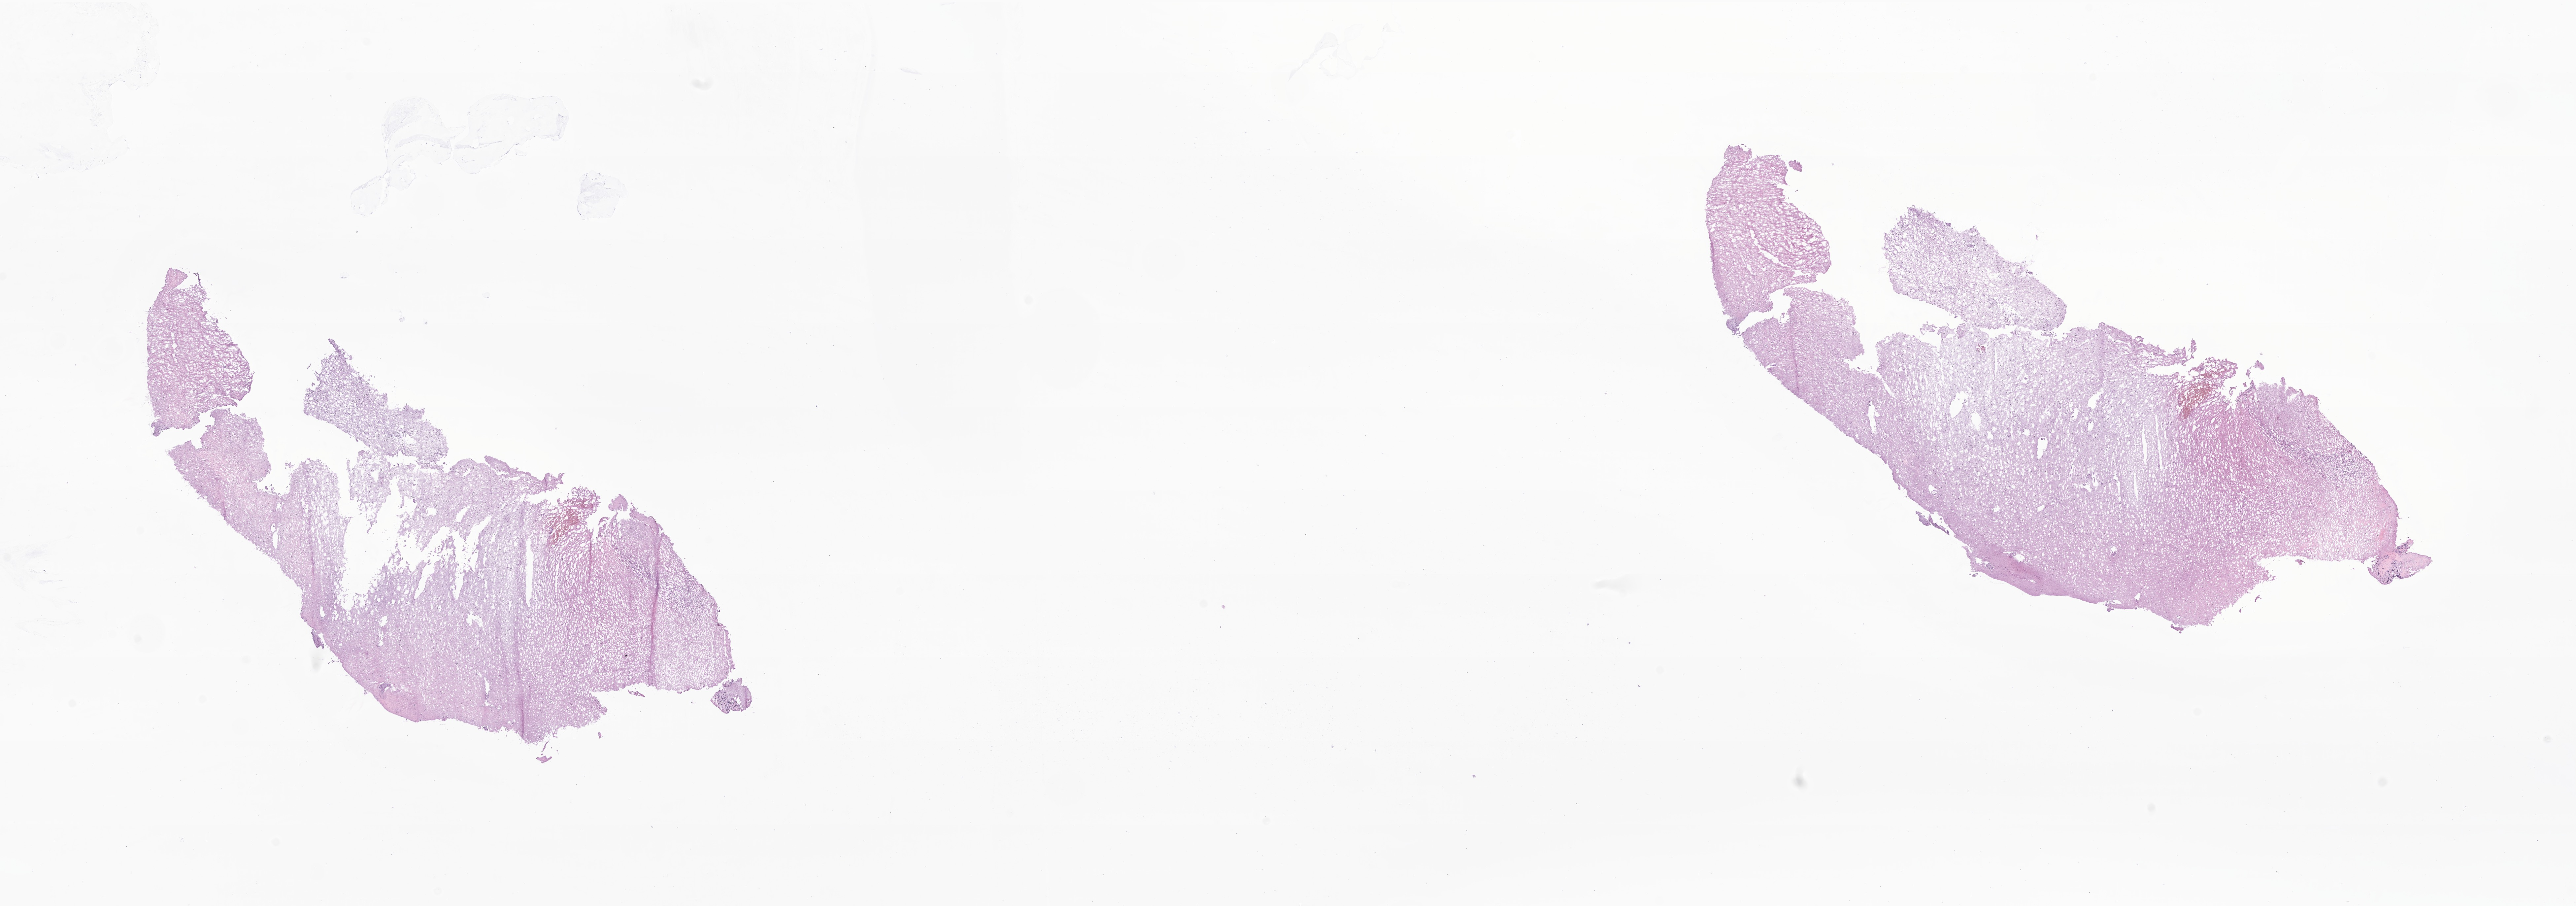
Digitized H&E-stained section of tumor tissue from the cerebellum — low-resolution overview of the scanned area, about 32.9 x 11.6 mm, frozen section. Patient: male, age 44 months (3 years 8 months).
- recorded diagnosis: Pilocytic astrocytoma